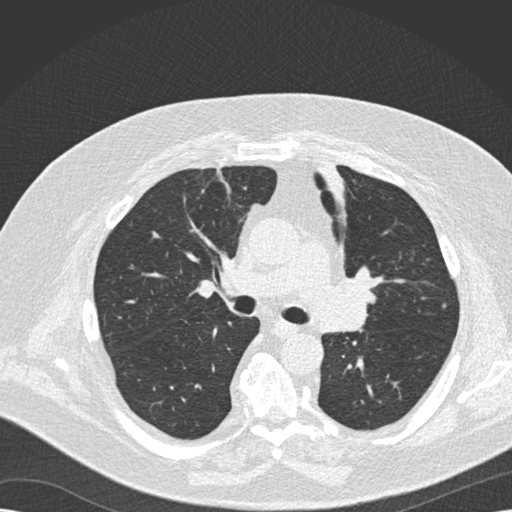
Low-dose screening chest CT, one axial slice. Reconstruction kernel B30f. Lung window (W 1500 / L -600 HU). 2 mm slice thickness. 512 × 512 image matrix, field of view 370 × 370 mm.
Structures marked on this image (outlined manually by an expert reader):
- lesion 1 (tumor, upper lobe of left lung): bounding box [x1, y1, x2, y2] px = [319, 163, 346, 196]